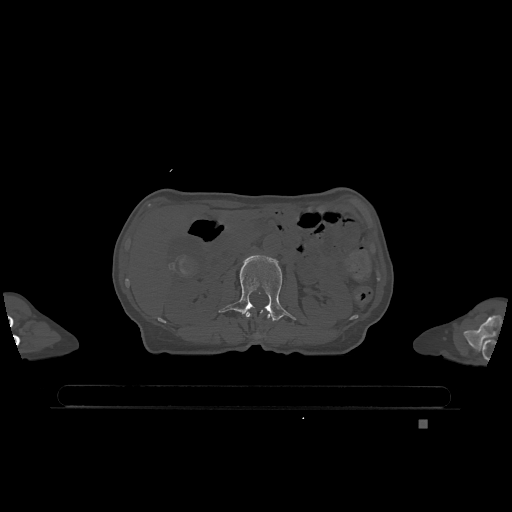
CT including the spine, one axial slice. Bone window (W 1800 / L 400 HU). 0.5 mm slice thickness. 512 × 512 image matrix. Patient: female, 74 years. Case-level facts recorded for this patient, not image findings: primary cancer: lung; vertebrae with lytic lesions (as recorded): T1, T4, T5, T6, L4, L5.
Annotated regions visible in this slice (semi-automatic segmentation, software-assisted and operator-edited):
- L1 vertebra: bounding box (x1, y1, x2, y2) in pixels: (241, 312, 270, 336)
- L2 vertebra: (219, 255, 296, 321)